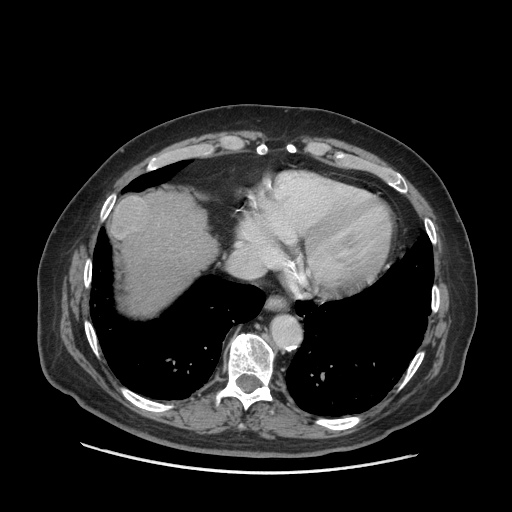
Contrast-enhanced abdominal CT (liver protocol), one axial slice. Position 63 of 77 along the scan axis. 140 kVp. Soft-tissue window (W 400 / L 40 HU). 512 × 512 image matrix, field of view 420 × 420 mm. From the clinical record (not read from this slice): diagnosis: hepatocellular carcinoma (patient treated with transarterial chemoembolisation; whether this scan precedes or follows treatment is not stated here); TNM stage (as recorded): Stage-I; Child-Pugh class: A; tumour differentiation: well differentiated; tumour nodularity: uninodular.
Annotated regions visible in this slice (semi-automatically segmented with operator editing):
- abdominal aorta: box from (x=272, y=317) to (x=301, y=346) px
- liver parenchyma outside the tumour (the mass and vessels are separate outlines, so this box may not span the whole liver): (x=110, y=192)–(x=216, y=314)
- mass: (x=111, y=196)–(x=149, y=239)